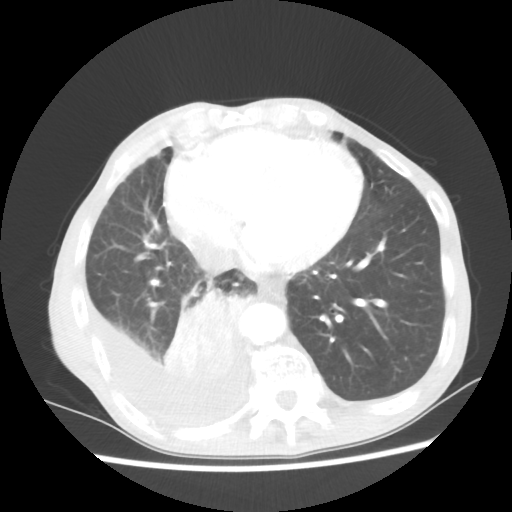
Chest CT, one axial slice. Slice 20 of 60 in the series (ordered by position). Lung window (W 1500 / L -600 HU). 5 mm slice thickness. 512 × 512 image matrix. Patient: male, 76 years. Case-level facts recorded for this patient, not image findings: clinical TNM (as recorded): T3 N3 M1a.
Outlined on this slice (rectangle marked by the reading radiologist):
- lung tumour (recorded histology: squamous cell carcinoma): bounding box [x1, y1, x2, y2] px = [162, 286, 243, 387]